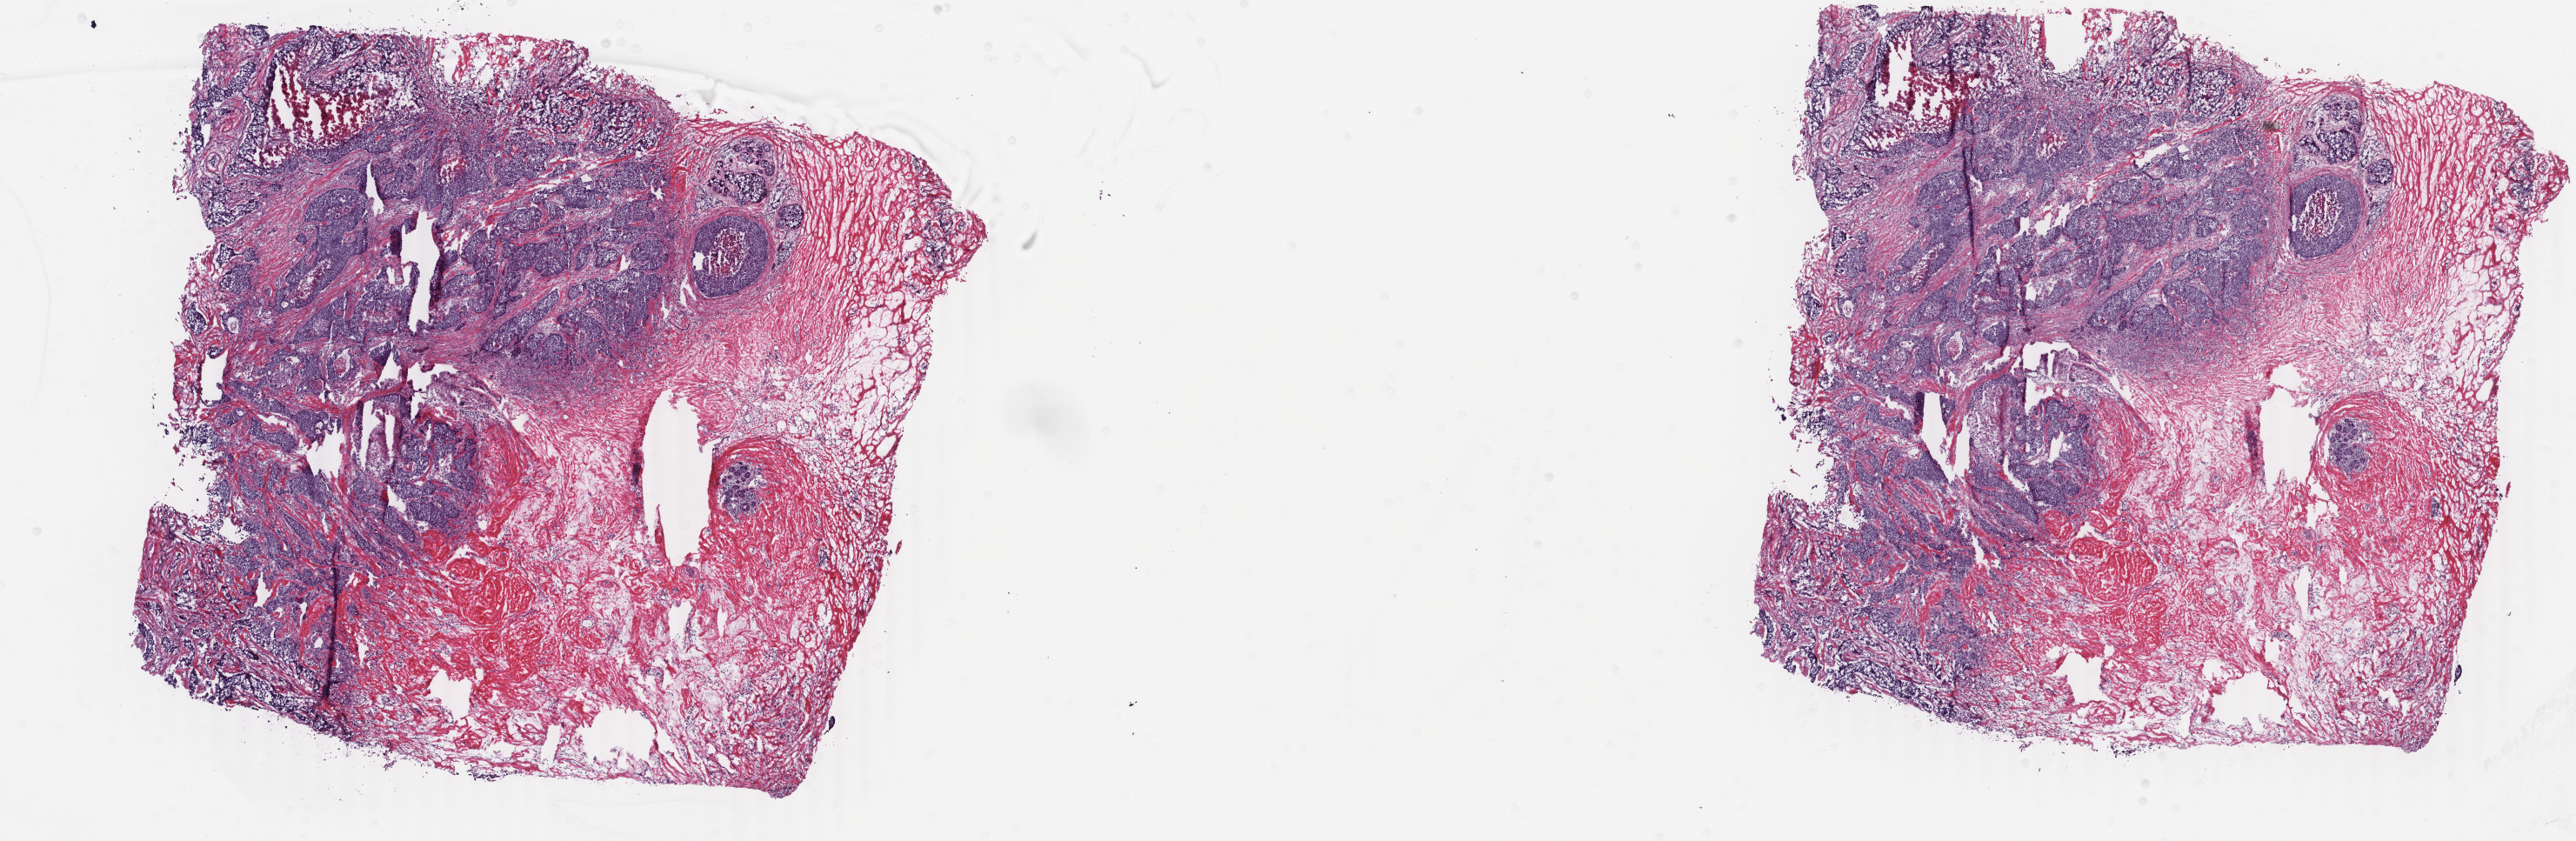
Whole-slide histology image, H&E-stained — low-resolution overview of the scanned area, about 23.6 x 7.7 mm (slide scanned at 40x), frozen section from the top of the tissue portion, primary tumour sample from the breast. Patient: female, age at initial diagnosis 51 years. Composition of this section per pathologist review: tumour cells 35%, tumour nuclei 70%, normal cells 2%, stromal cells 43%, necrosis 20%. Infiltration values recorded for this section: lymphocyte infiltration 3%, monocyte infiltration 0%, neutrophil infiltration 0%.
Pathologic diagnosis: Infiltrating duct carcinoma, NOS. Lymph nodes positive (case pathology): 9 of 11 examined. Laterality: right.